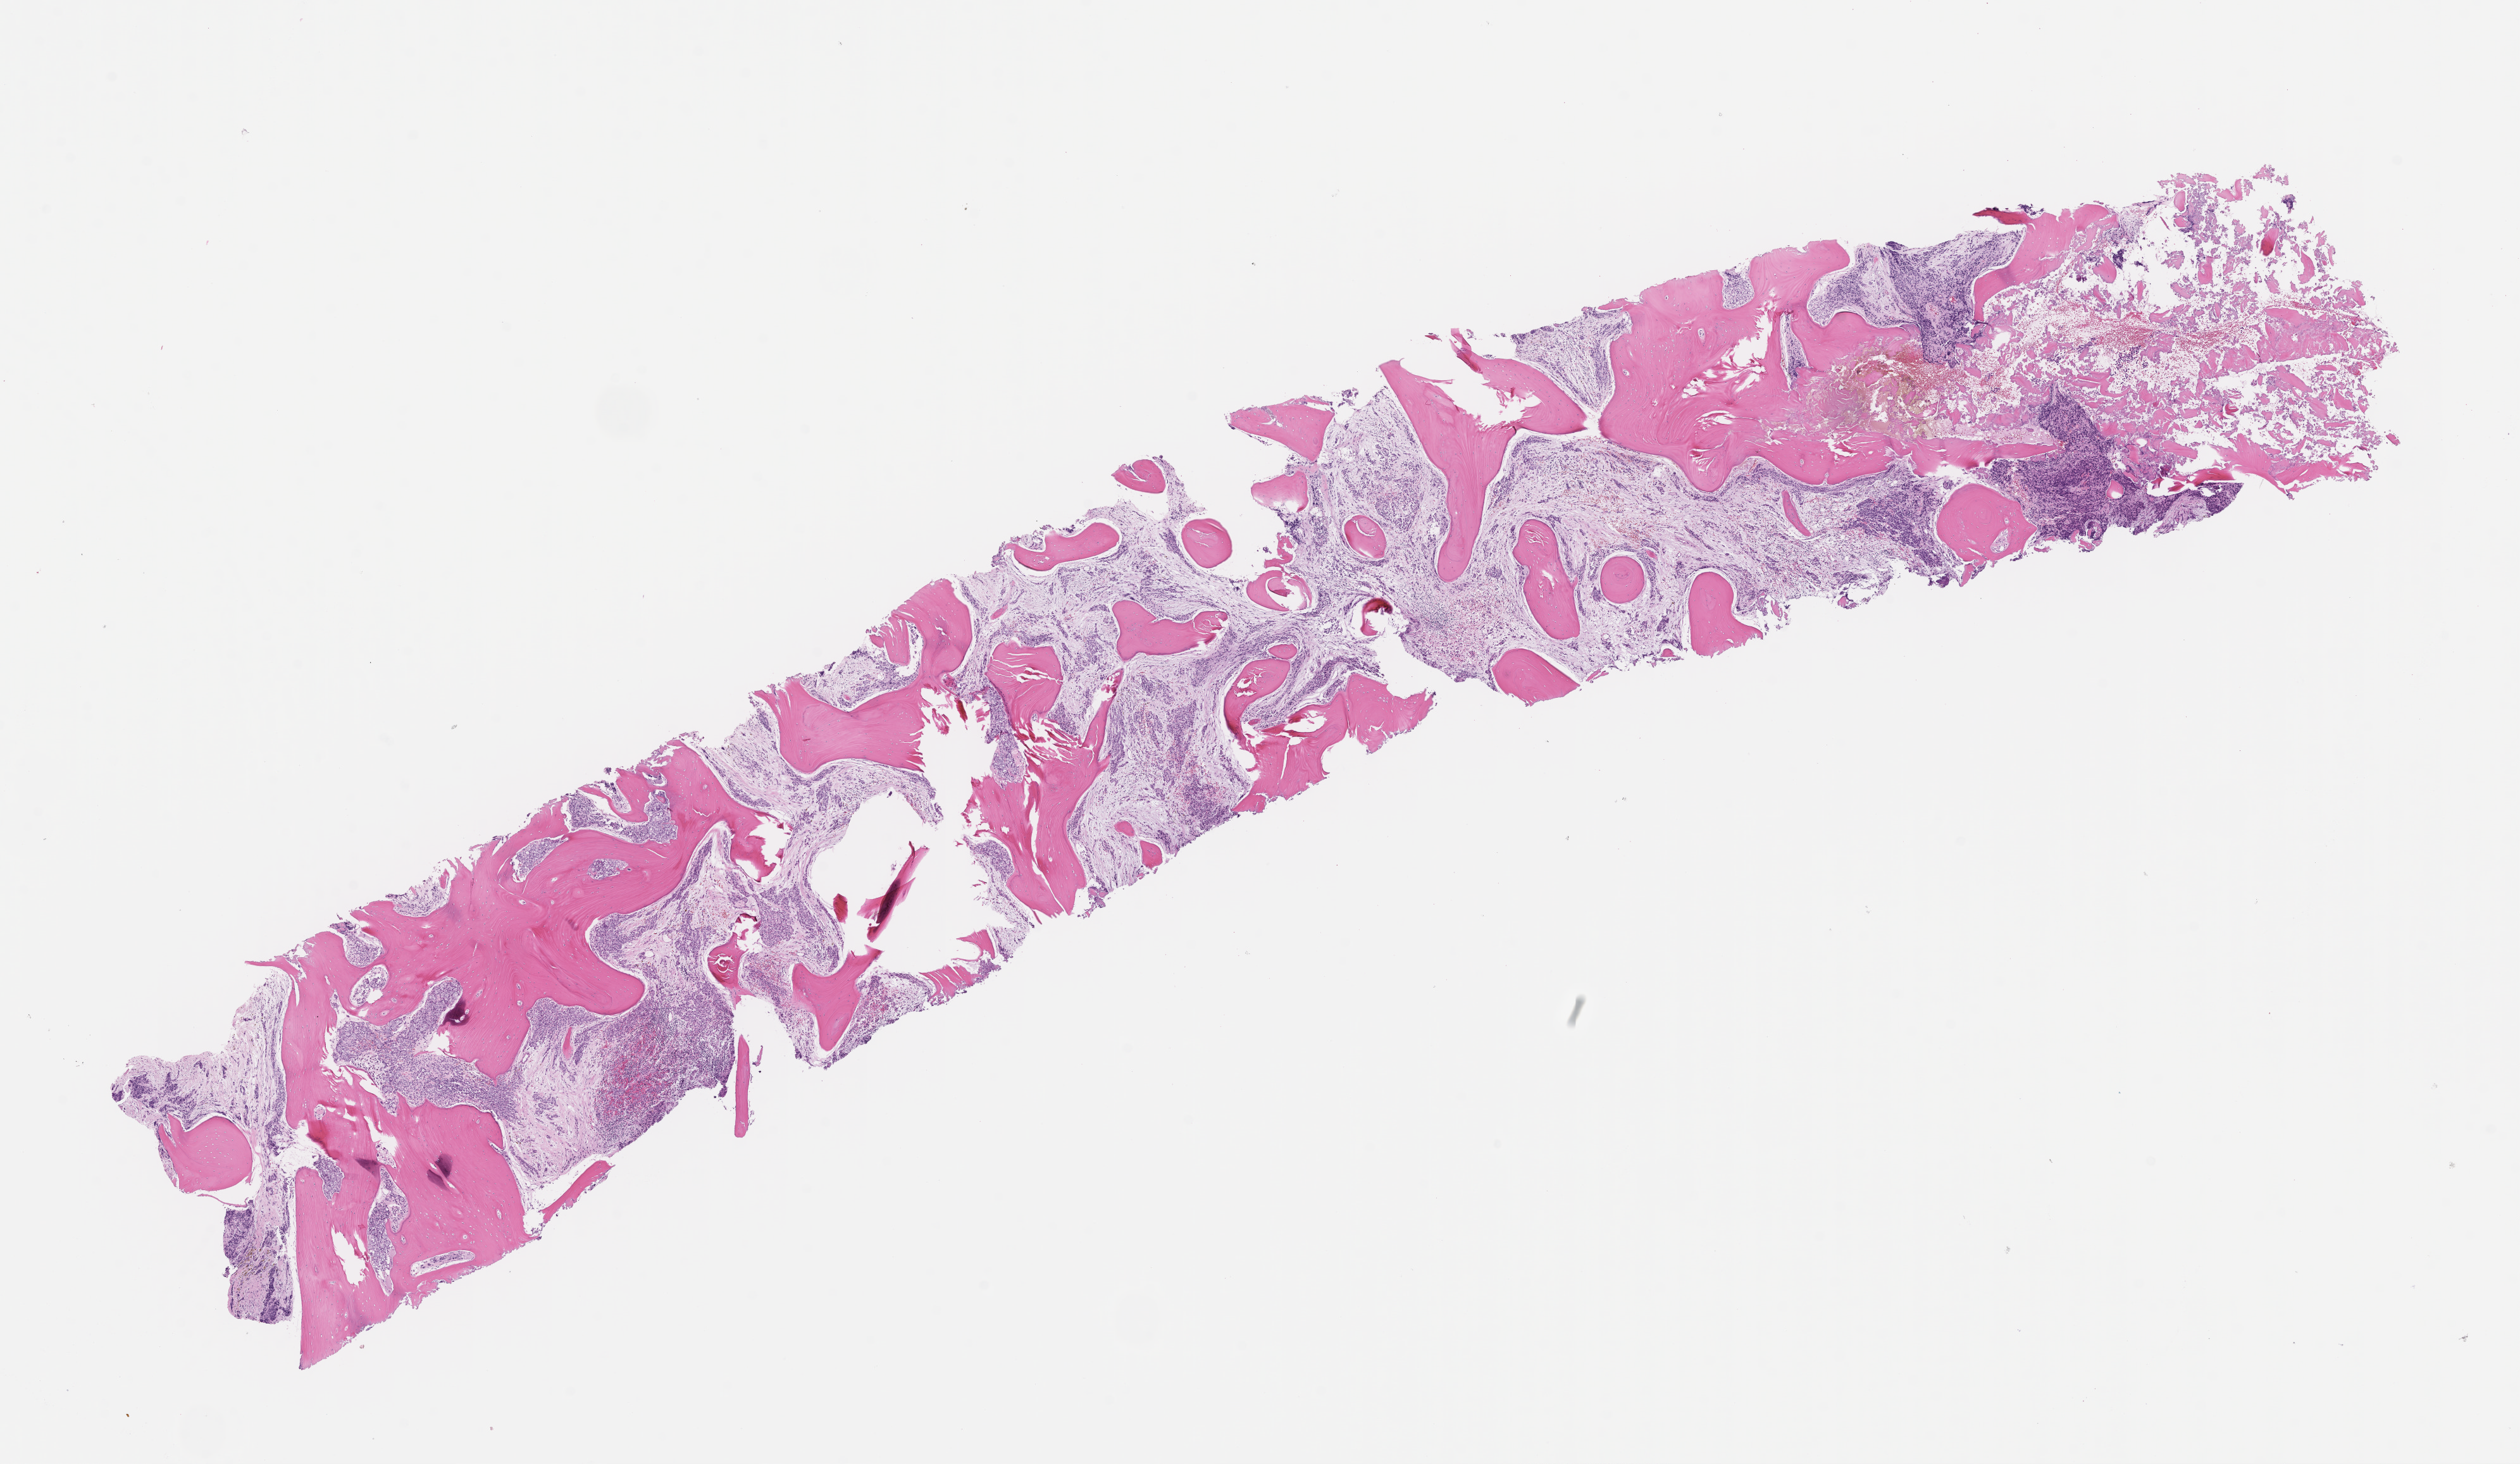
Whole-slide image, hematoxylin and eosin (H&E) stain, a low-resolution overview of the entire scanned area, about 16.1 x 9.3 mm. Formalin-fixed, paraffin-embedded (FFPE) tissue. Patient sex: male.
This section: metastatic tumor tissue. Primary diagnosis of the patient: Prostate Carcinoma.